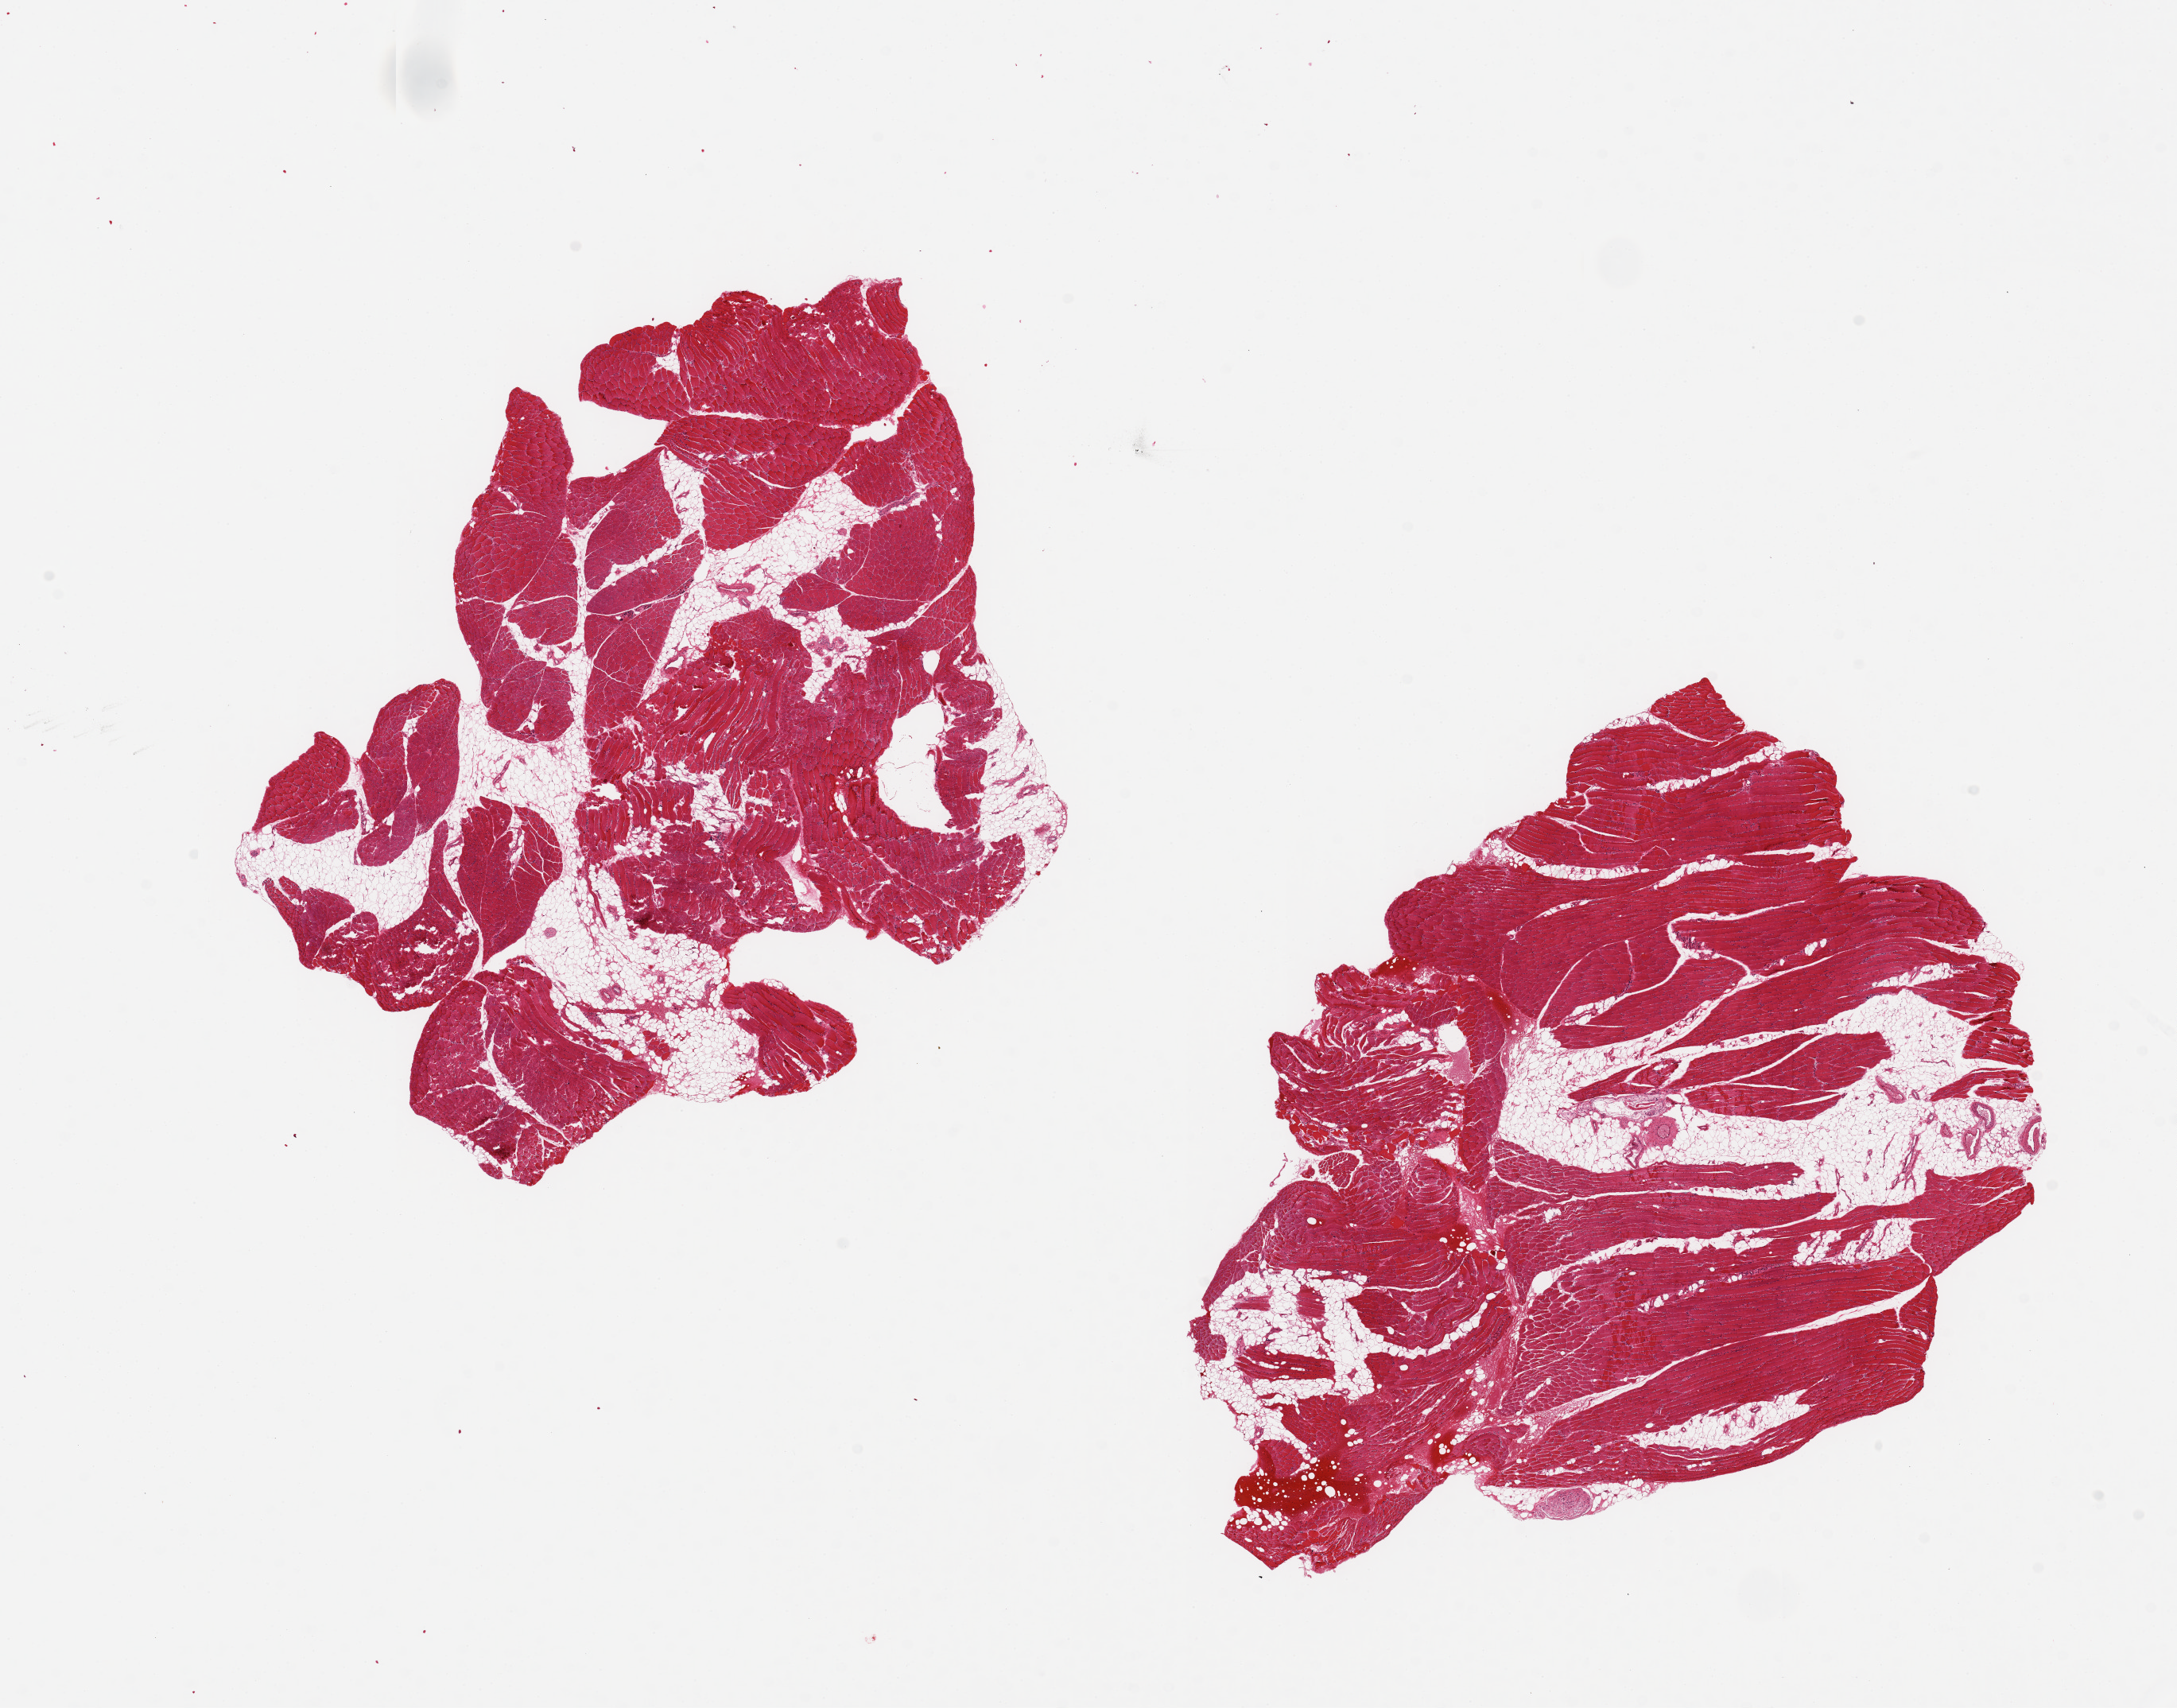
Hematoxylin and eosin (H&E) whole-slide image, shown as a low-resolution overview of the whole scanned area (about 21.7 x 17.0 mm, acquisition: 20x scan), PAXgene-fixed, paraffin-embedded tissue, target tissue: skeletal muscle, tissue donor sample. Donor: male.
Reviewer comment on this tissue sample: 2 pieces, ~8x8mm. ~15-20% interstitial fat.